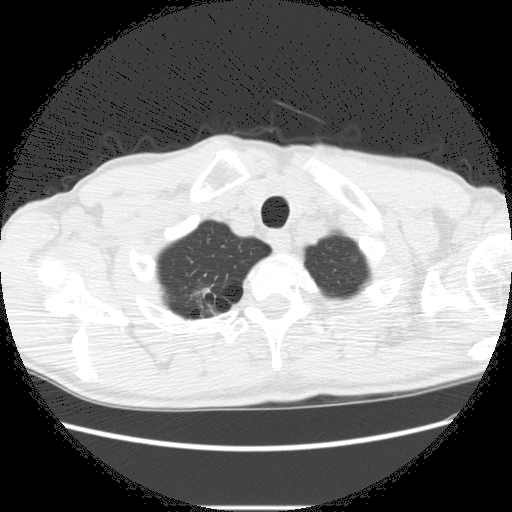
Low-dose screening chest CT, one axial slice. Position 263 of 282 along the scan axis. 120 kVp. Lung window (W 1500 / L -600 HU). 512 × 512 image matrix.
Annotated regions visible in this slice (expert manual segmentation):
- lesion 2 (nodule, upper lobe of right lung): bounding box (x1, y1, x2, y2) in pixels: (199, 287, 216, 305)